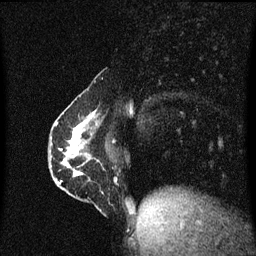
Breast MRI (dynamic contrast-enhanced), one sagittal slice; dynamic contrast-enhanced series, image 2 of 3 at this slice position (ordered by acquisition); 1.5 T; TE 4.2 ms, TR 8.4 ms; 2 mm slice thickness; 256 × 256 image matrix, field of view 200 × 200 mm. Patient: female, 40 years.
Structures marked on this image (semi-automatic segmentation, software-assisted and operator-edited):
- analysis volume of interest (the breast-tissue region the enhancement analysis was run in; not a lesion): box from (x=57, y=110) to (x=112, y=191) px
- tumour enhancement mask (voxels above the 70 % enhancement threshold inside the analysis volume of interest): (x=57, y=112)–(x=95, y=183)